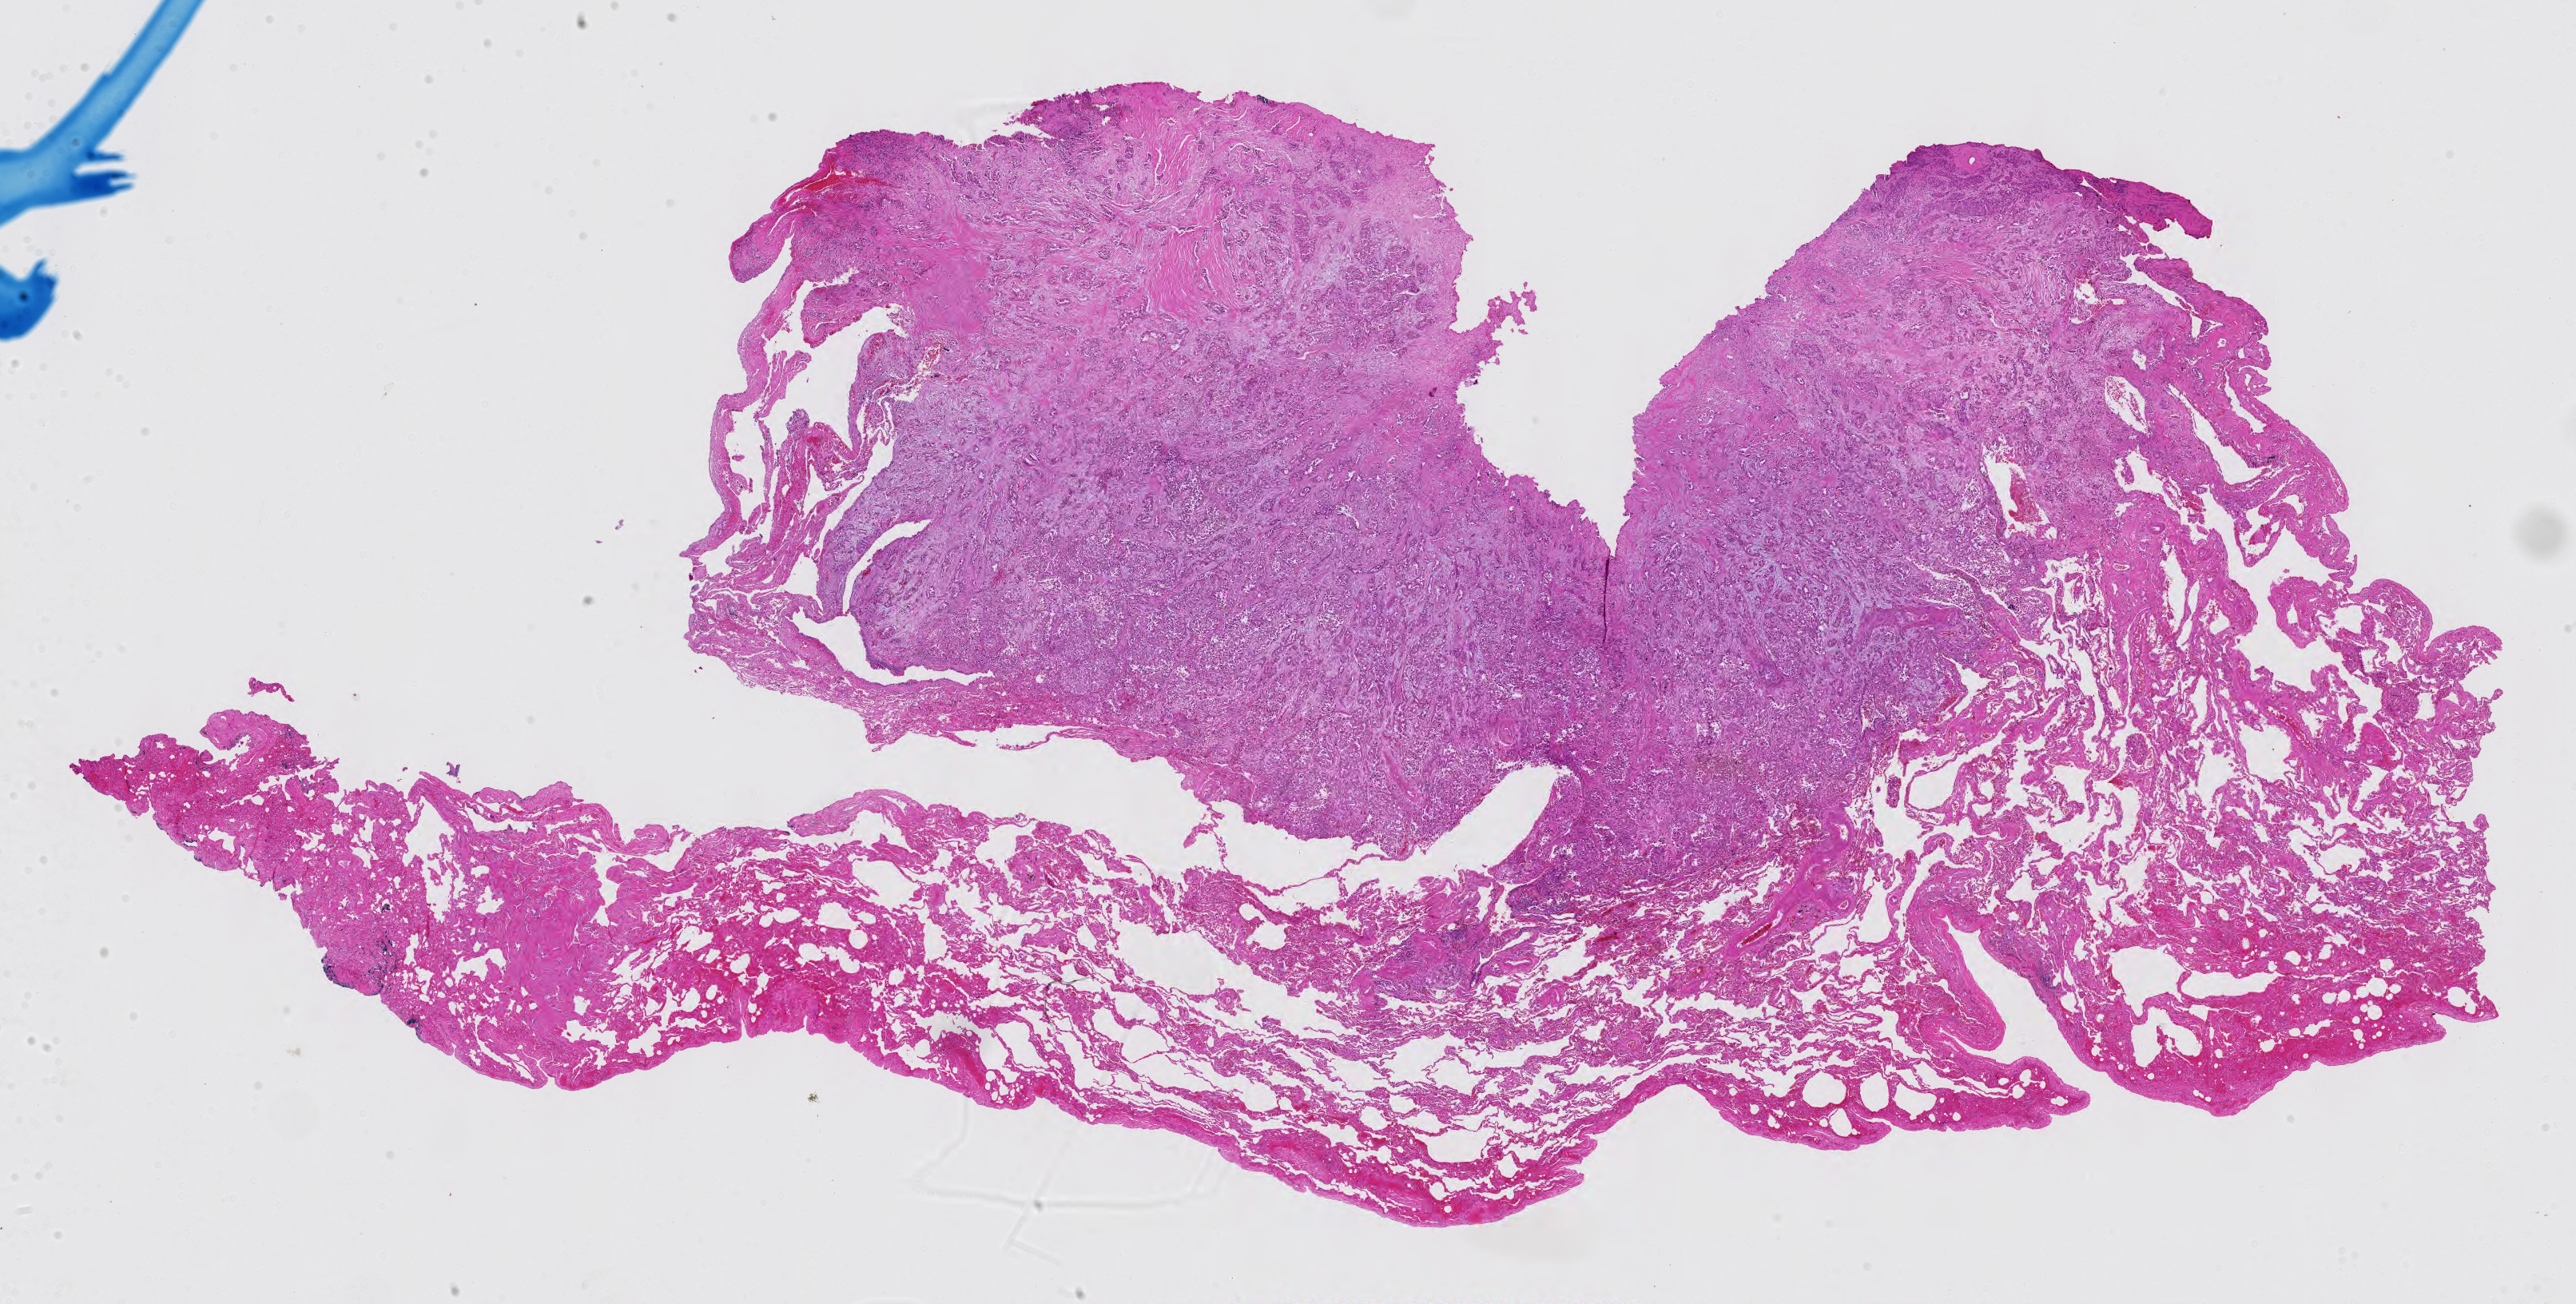
Digitized H&E tissue section (whole slide), shown as a low-resolution overview of the whole scanned area (about 23.4 x 11.8 mm, from a 40x scan). Formalin-fixed paraffin-embedded (FFPE) diagnostic section. Sample: primary tumour, lung. Female, age 63 years at initial diagnosis.
Pathologic diagnosis: Adenocarcinoma with mixed subtypes (upper lobe, lung). AJCC pathologic stage: IA (7th edition).